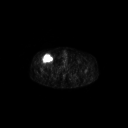
FDG PET of an extremity soft-tissue mass (from a PET/CT study), one axial slice; position 302 of 311 along the scan axis; 3.27 mm slice thickness; 128 × 128 image matrix, field of view 700 × 700 mm. Male patient, age 56 years. Case-level facts recorded for this patient, not image findings: histological type: pleiomorphic leiomyosarcoma; grade: intermediate; site of the primary tumour: right thigh.
Outlined on this slice (expert contour drawn on MRI and transferred to this co-registered scan by the dataset authors):
- gross tumour volume including surrounding oedema: bounding box [x1, y1, x2, y2] px = [41, 53, 53, 63]
- gross tumour volume (mass): [42, 55, 52, 63]